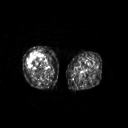
FDG PET of an extremity soft-tissue mass (from a PET/CT study), one axial slice. Position 216 of 311 along the scan axis. 3.27 mm slice thickness. 128 × 128 image matrix, field of view 500 × 500 mm. Patient: female, 57 years. Case-level facts recorded for this patient, not image findings: histological type: pleiomorphic undifferentiated sarcoma; grade: high; site of the primary tumour: right quadricep.
Structures marked on this image (expert contour drawn on MRI and transferred to this co-registered scan by the dataset authors):
- tumour plus oedema (research contour): bounding box <27,52,41,66> (left, top, right, bottom; pixels)